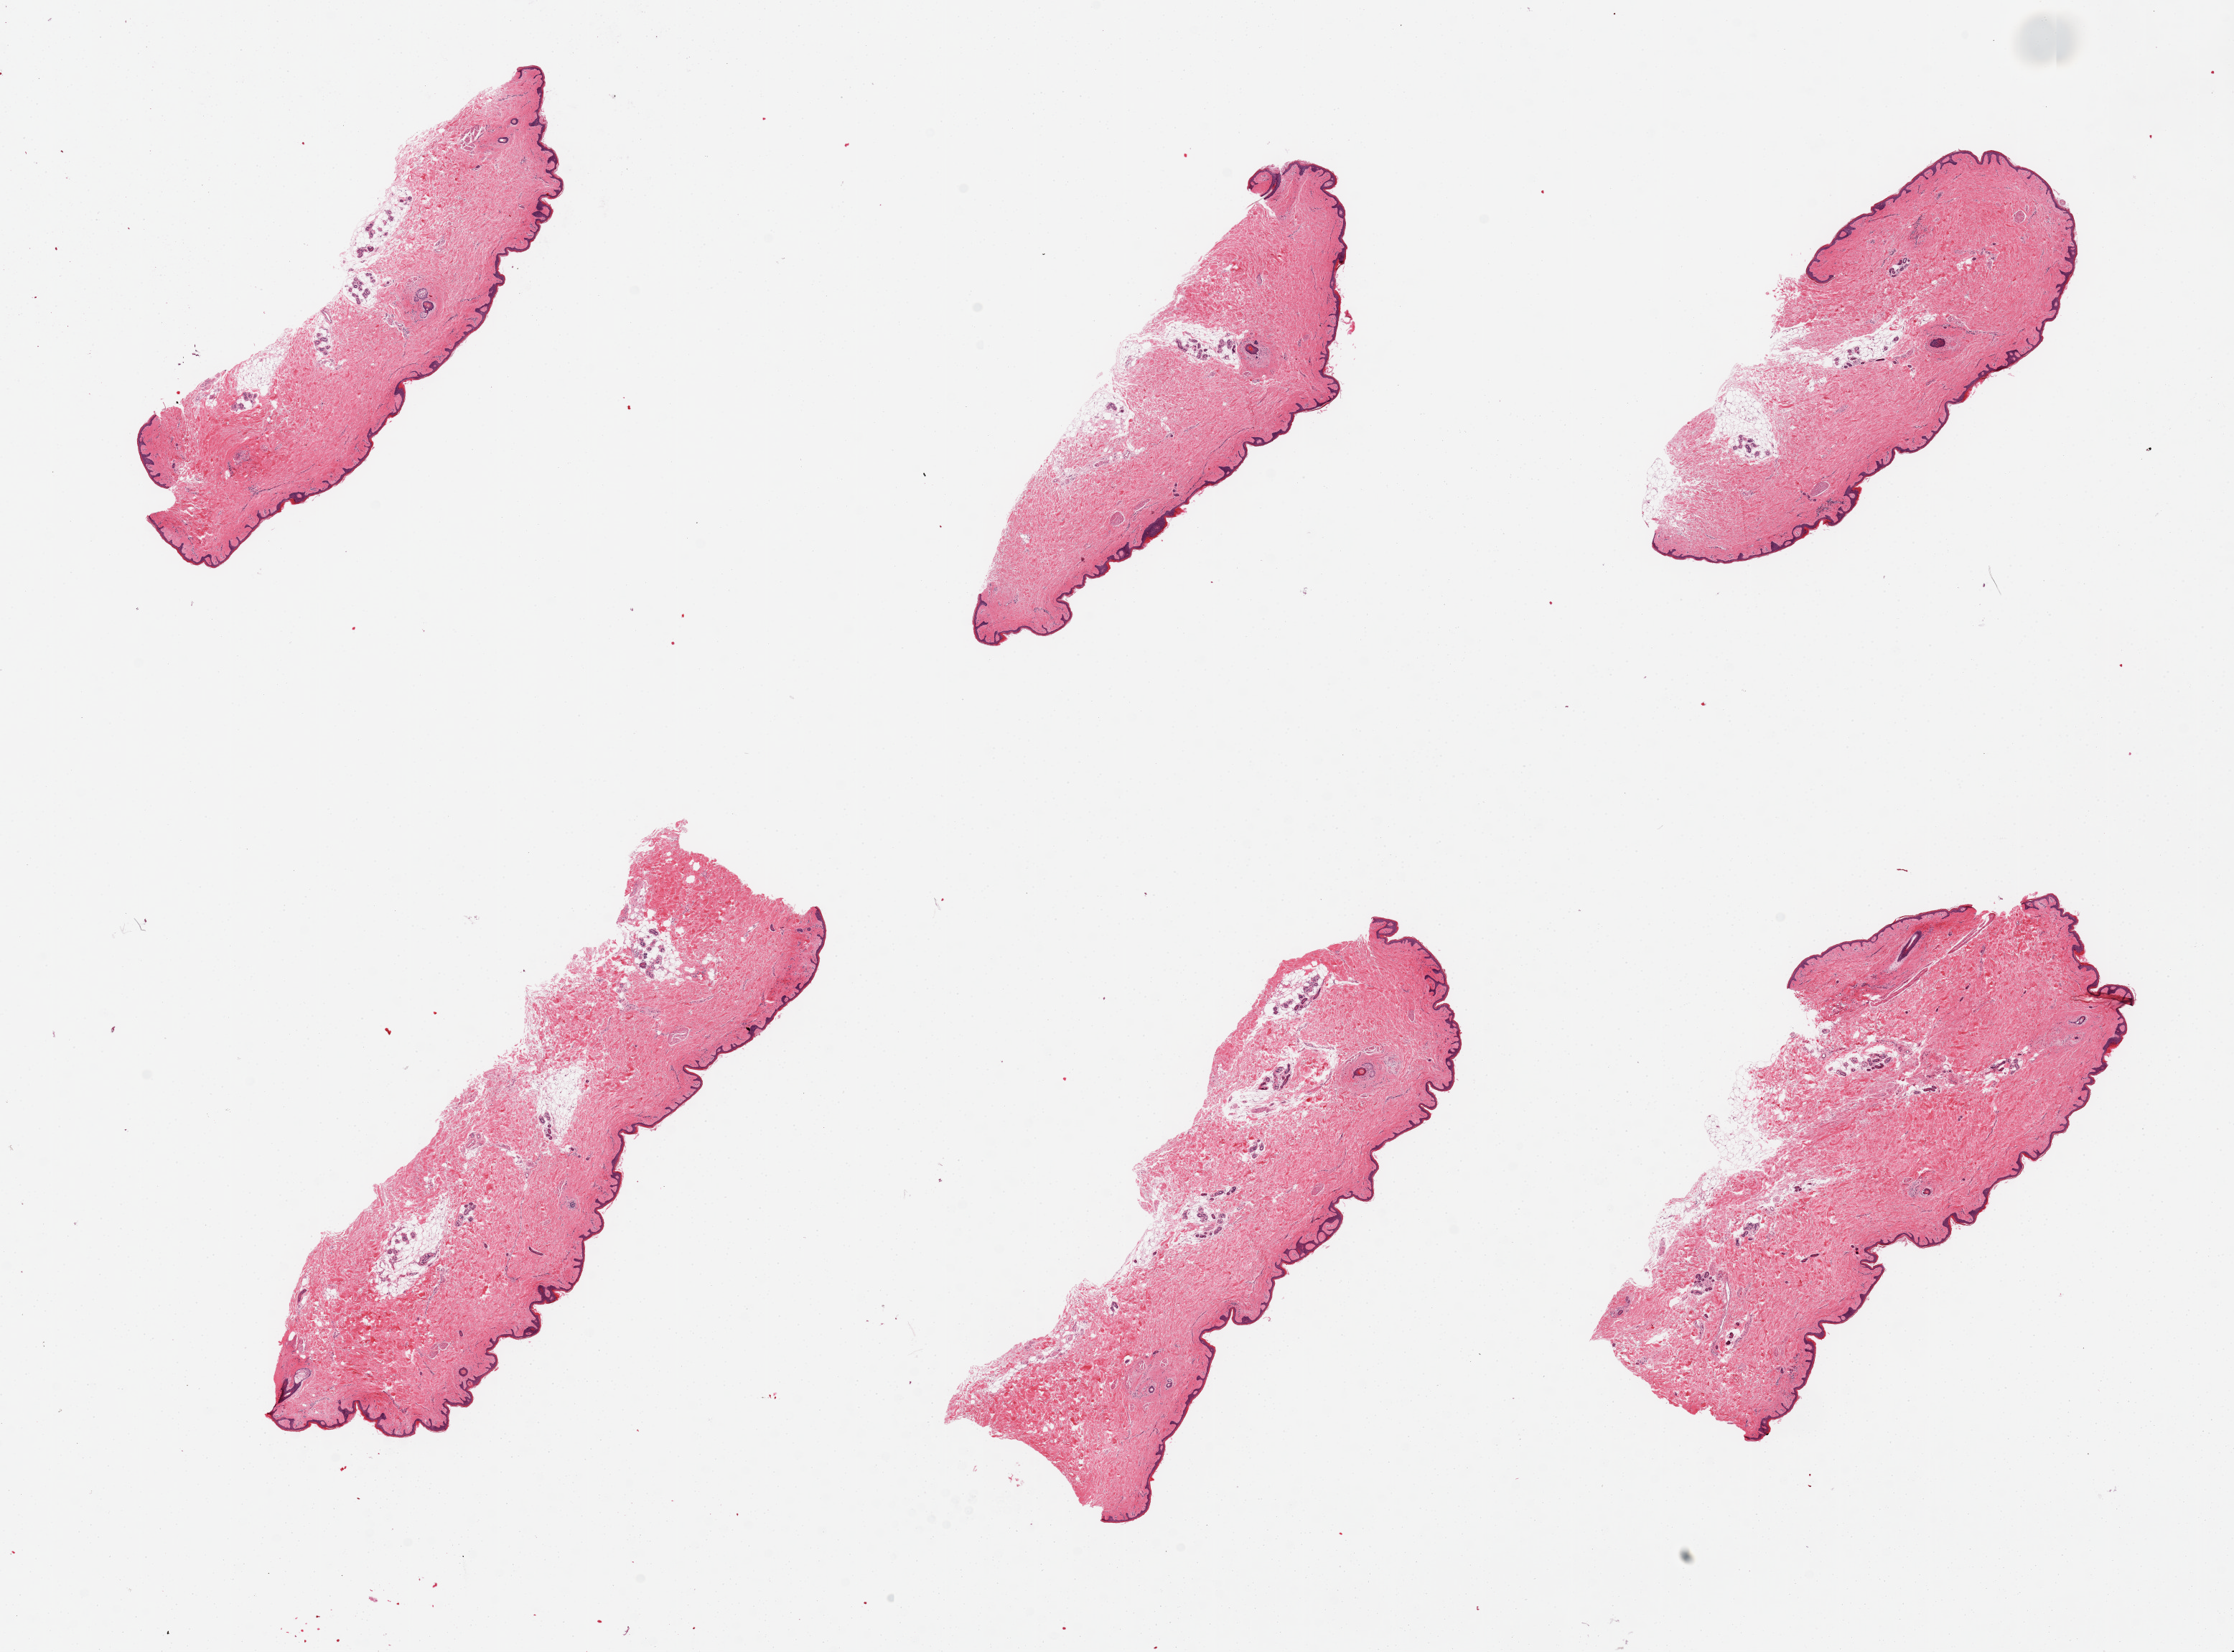
Hematoxylin and eosin (H&E) whole-slide image, brightfield, whole scanned area (about 24.6 x 18.2 mm) shown as a low-resolution overview. PAXgene-fixed, paraffin-embedded tissue. Target tissue: skin of suprapubic region. Tissue donor sample. Donor: female.
Pathologist's review note for this sample: 6 pieces, minimal adherent fat; squamous epithelium is ~30 microns.